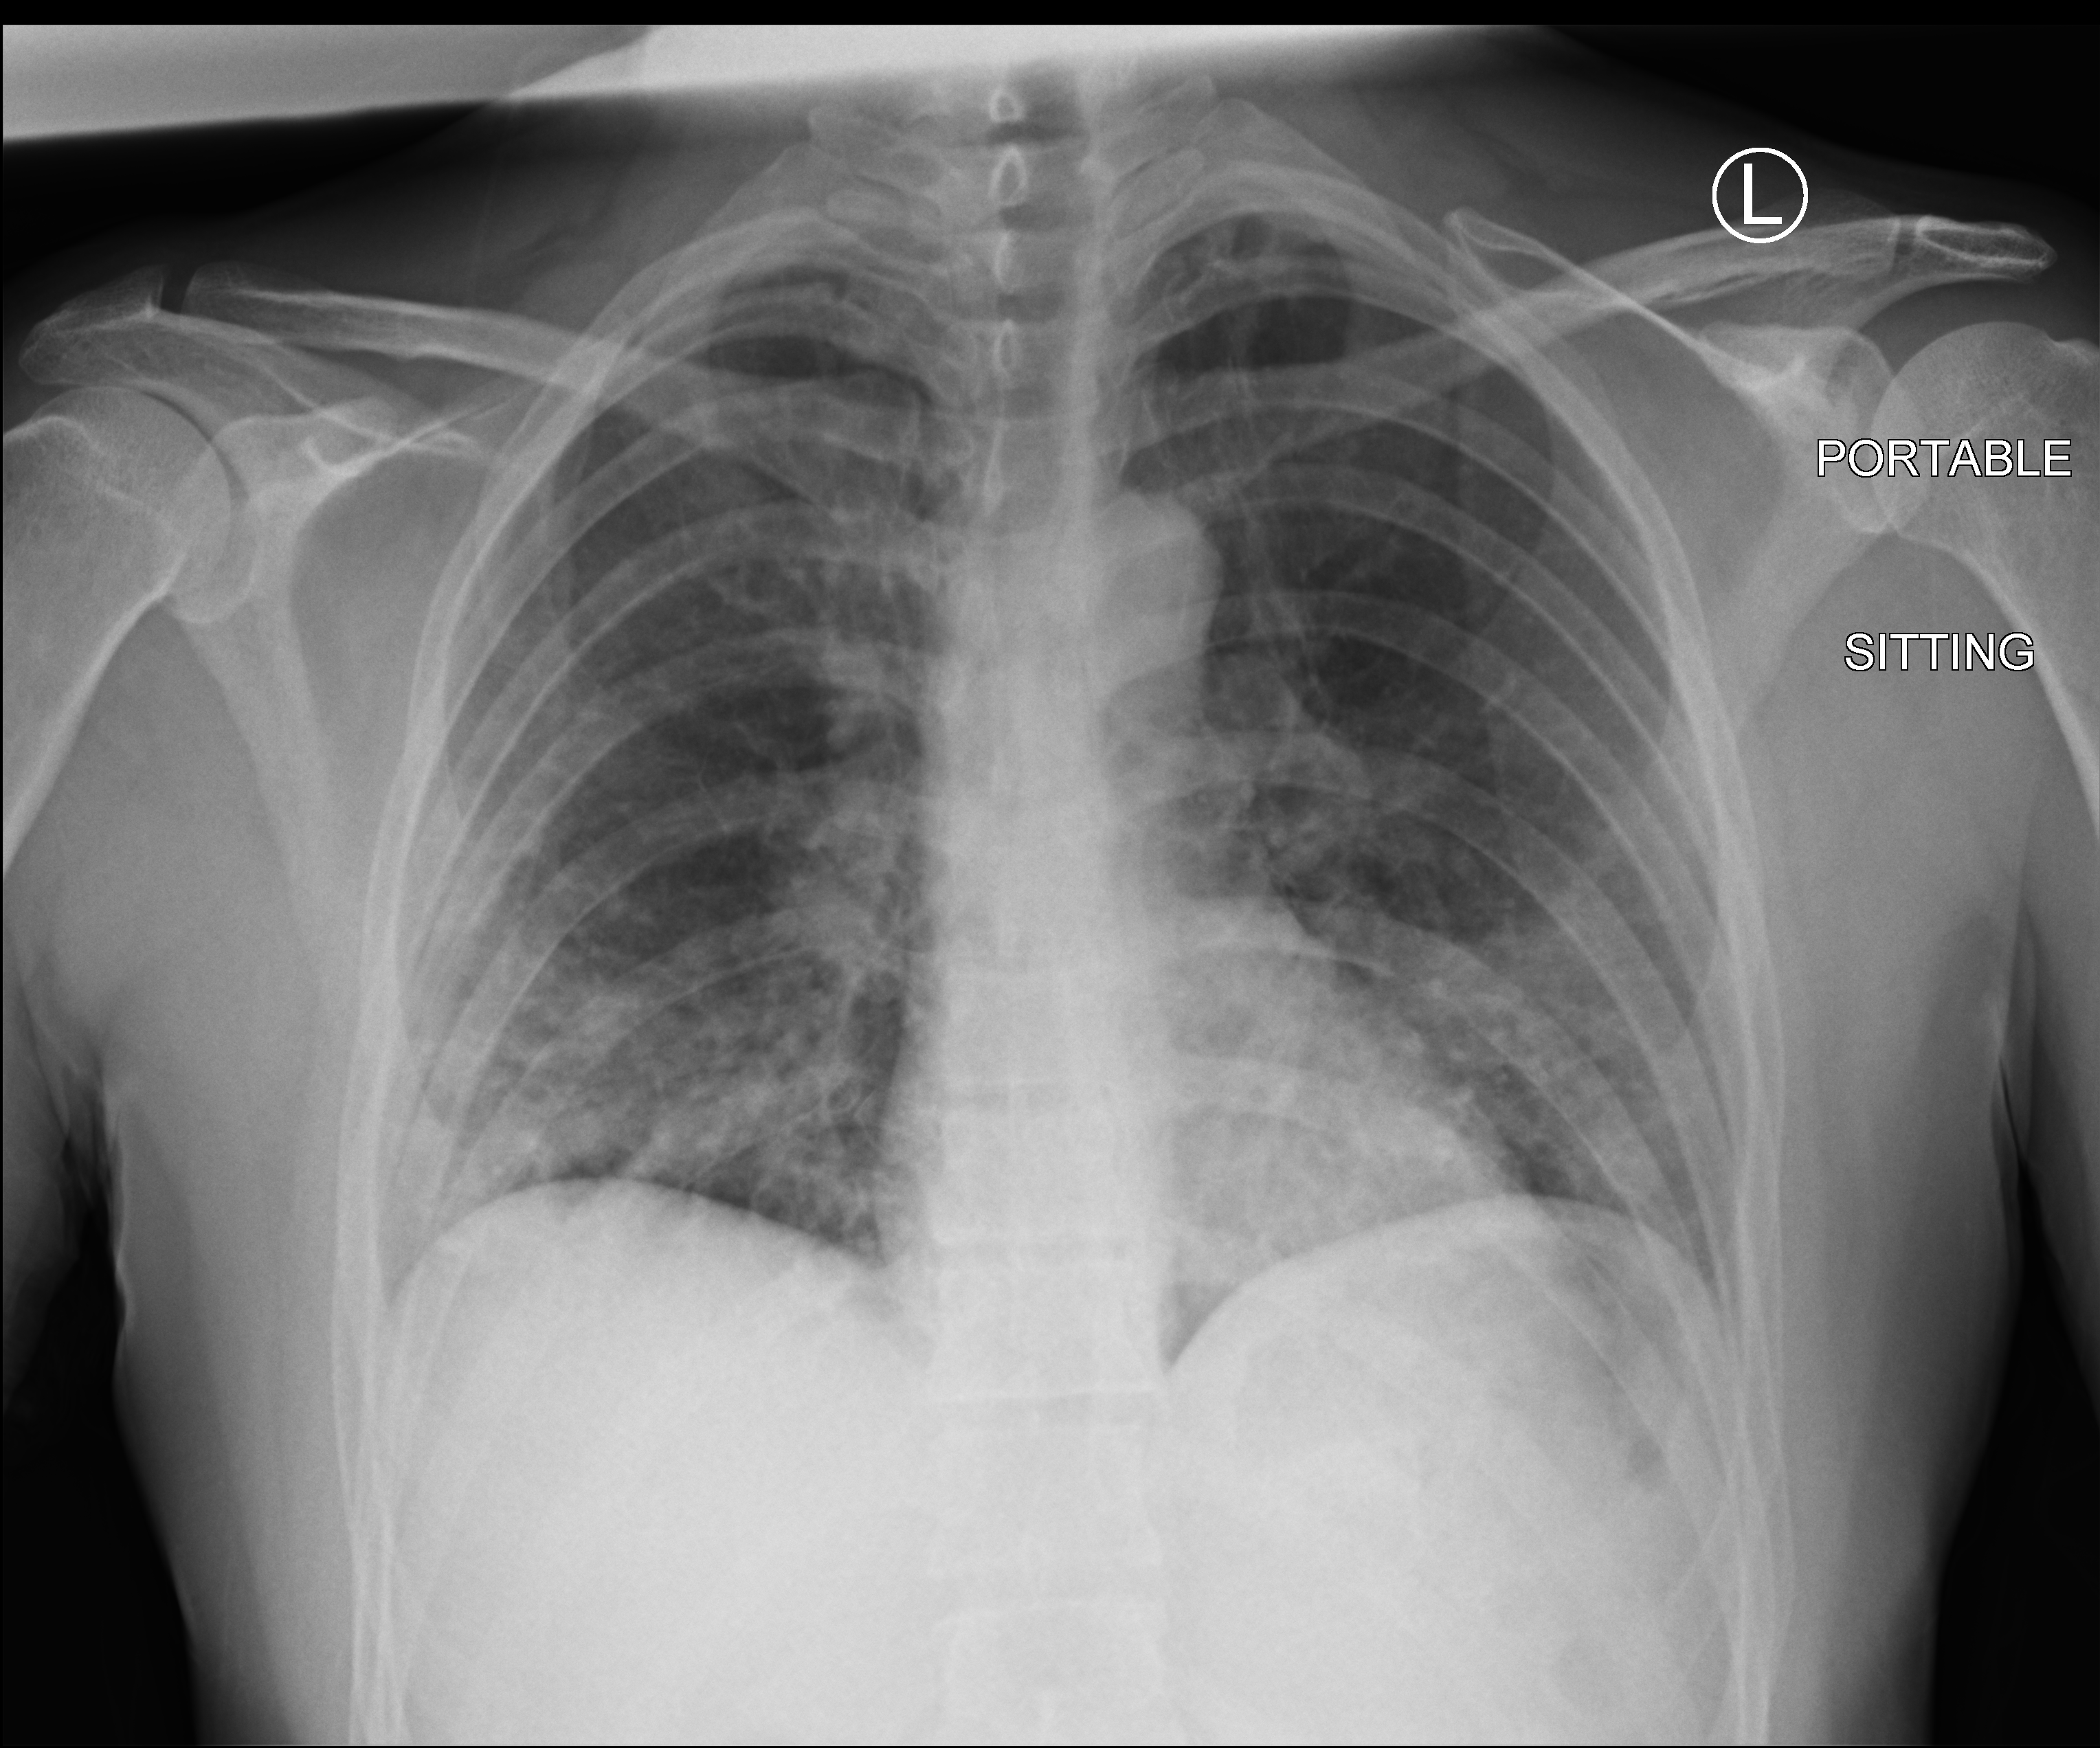
Portable chest radiograph; anteroposterior (AP) projection. Patient hospitalised with COVID-19; male, aged 18–59 years.
Hospital-stay facts (about this admission, not read from this image; timing relative to this image not recorded):
- admitted to intensive care during this hospital stay: no
- smoking status (admission record): never
- mechanically ventilated during this hospital stay: no